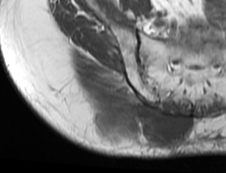
MRI of an extremity soft-tissue mass, one axial slice; slice 51 of 73 in the series (ordered by position); MR volume resampled by the dataset authors to the PET/CT grid (not the native acquisition matrix); 226 × 173 image matrix, field of view 221 × 169 mm. Female patient. From the clinical record (not read from this slice): histological type: spindle cell suggestive of myxofibrosarcoma; grade: intermediate; site of the primary tumour: right buttock.
Outlined on this slice (expert contour drawn on MRI and transferred to this co-registered scan by the dataset authors):
- gross tumour volume (mass): bounding box (x1, y1, x2, y2) in pixels: (88, 101, 190, 148)